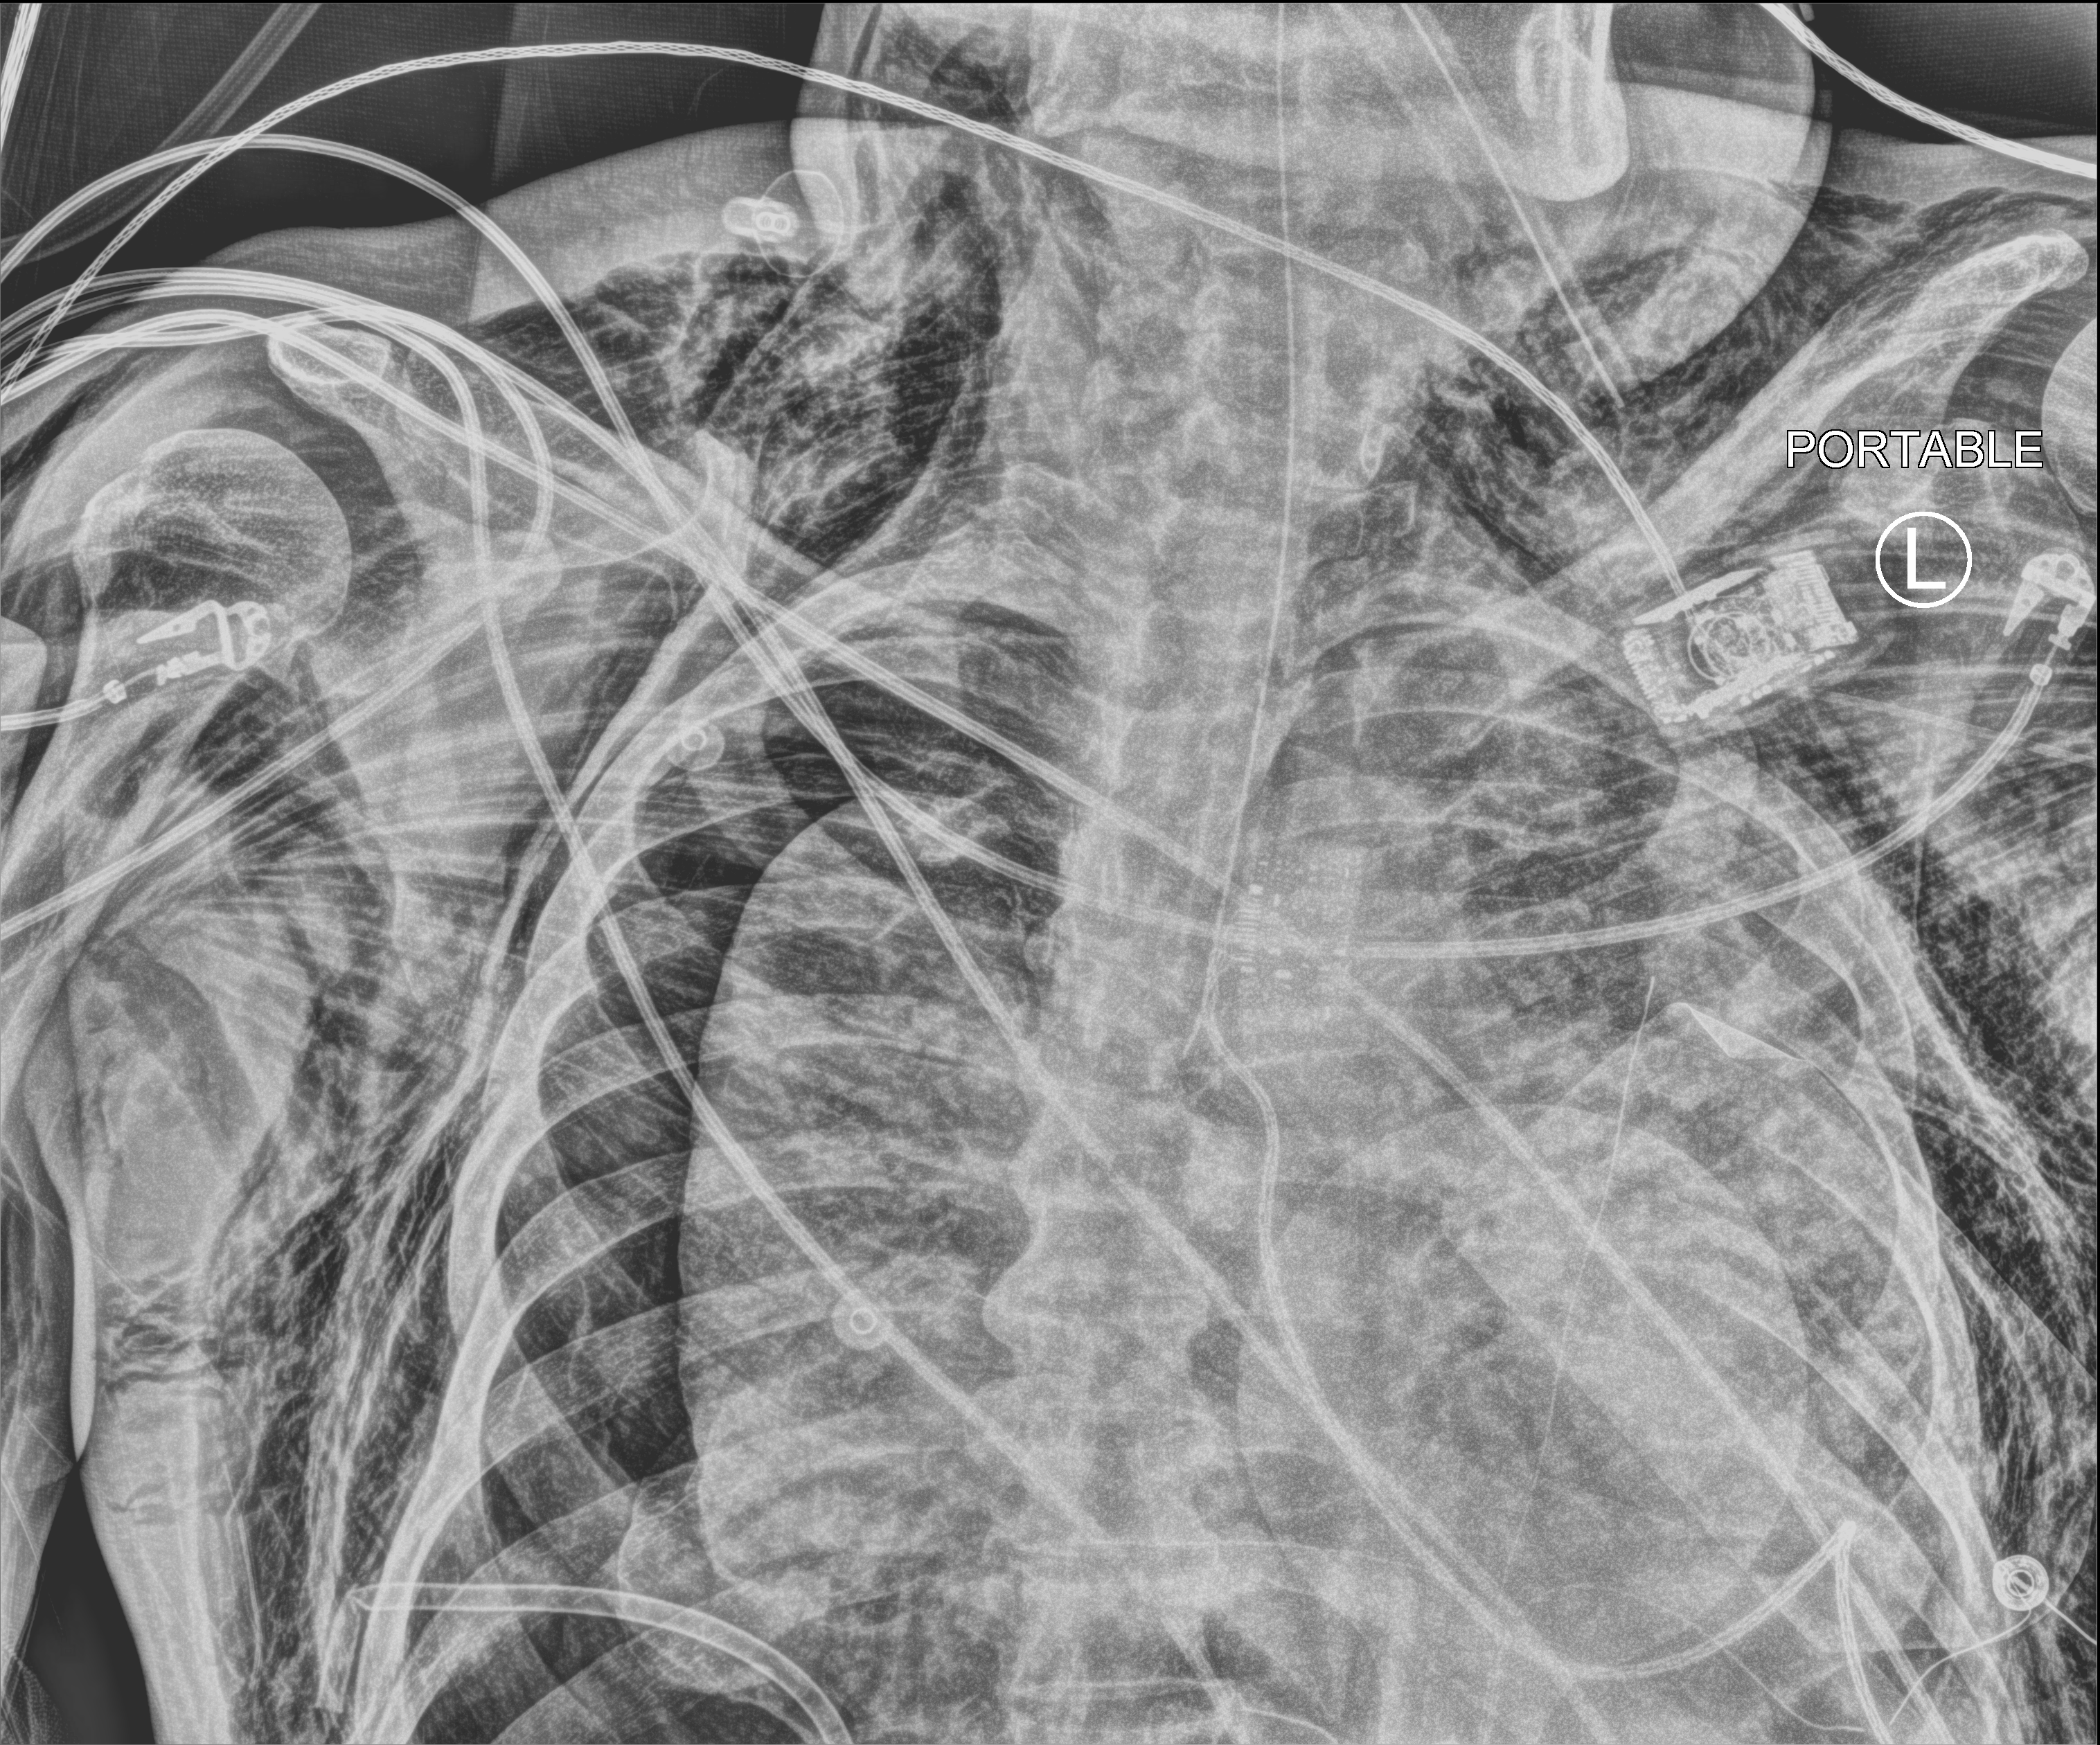
Portable chest radiograph, anteroposterior (AP) projection. Male patient hospitalised with COVID-19, age 75–90 years.
Hospital-stay facts (about this admission, not read from this image; timing relative to this image not recorded): admitted to intensive care during this hospital stay: yes.